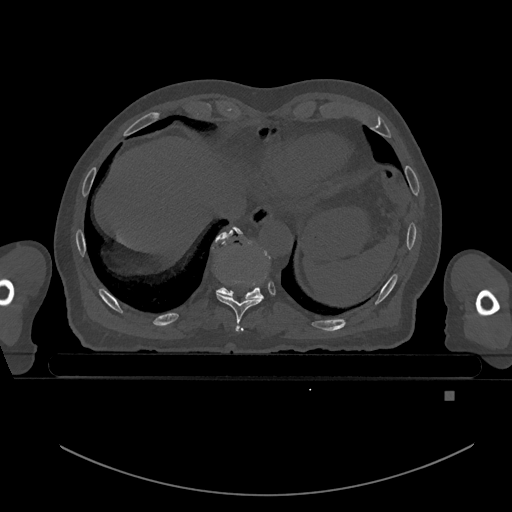
CT including the spine, one axial slice. Slice 125 of 969 in the series (ordered by position). Bone window (W 1800 / L 400 HU). 0.5 mm slice thickness. 512 × 512 image matrix, field of view 456 × 456 mm. Patient: male, 82 years. Case-level facts recorded for this patient, not image findings: primary cancer: prostate; vertebrae with lytic lesions (as recorded): T11, T9, T8, T2.
Outlined on this slice (semi-automatic segmentation, software-assisted and operator-edited):
- T10 vertebra: bounding box [x1, y1, x2, y2] px = [218, 226, 268, 298]
- T9 vertebra: [213, 230, 263, 332]